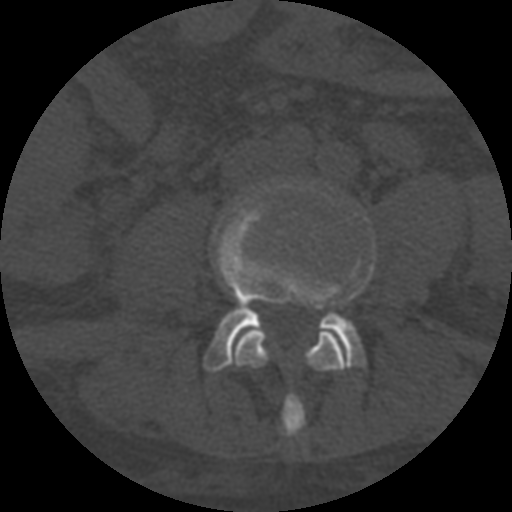
CT including the spine, one axial slice. Position 219 of 708 along the scan axis. Reconstruction kernel STANDARD. One of 3 acquisitions stored at this slice position. Bone window (W 1800 / L 400 HU). 512 × 512 image matrix. Patient age 55 years. Case-level facts recorded for this patient, not image findings: primary cancer: colon.
Annotated regions visible in this slice (semi-automatically segmented with operator editing):
- L3 vertebra: bounding box <233,329,348,436> (left, top, right, bottom; pixels)
- L4 vertebra: <203,197,364,372>